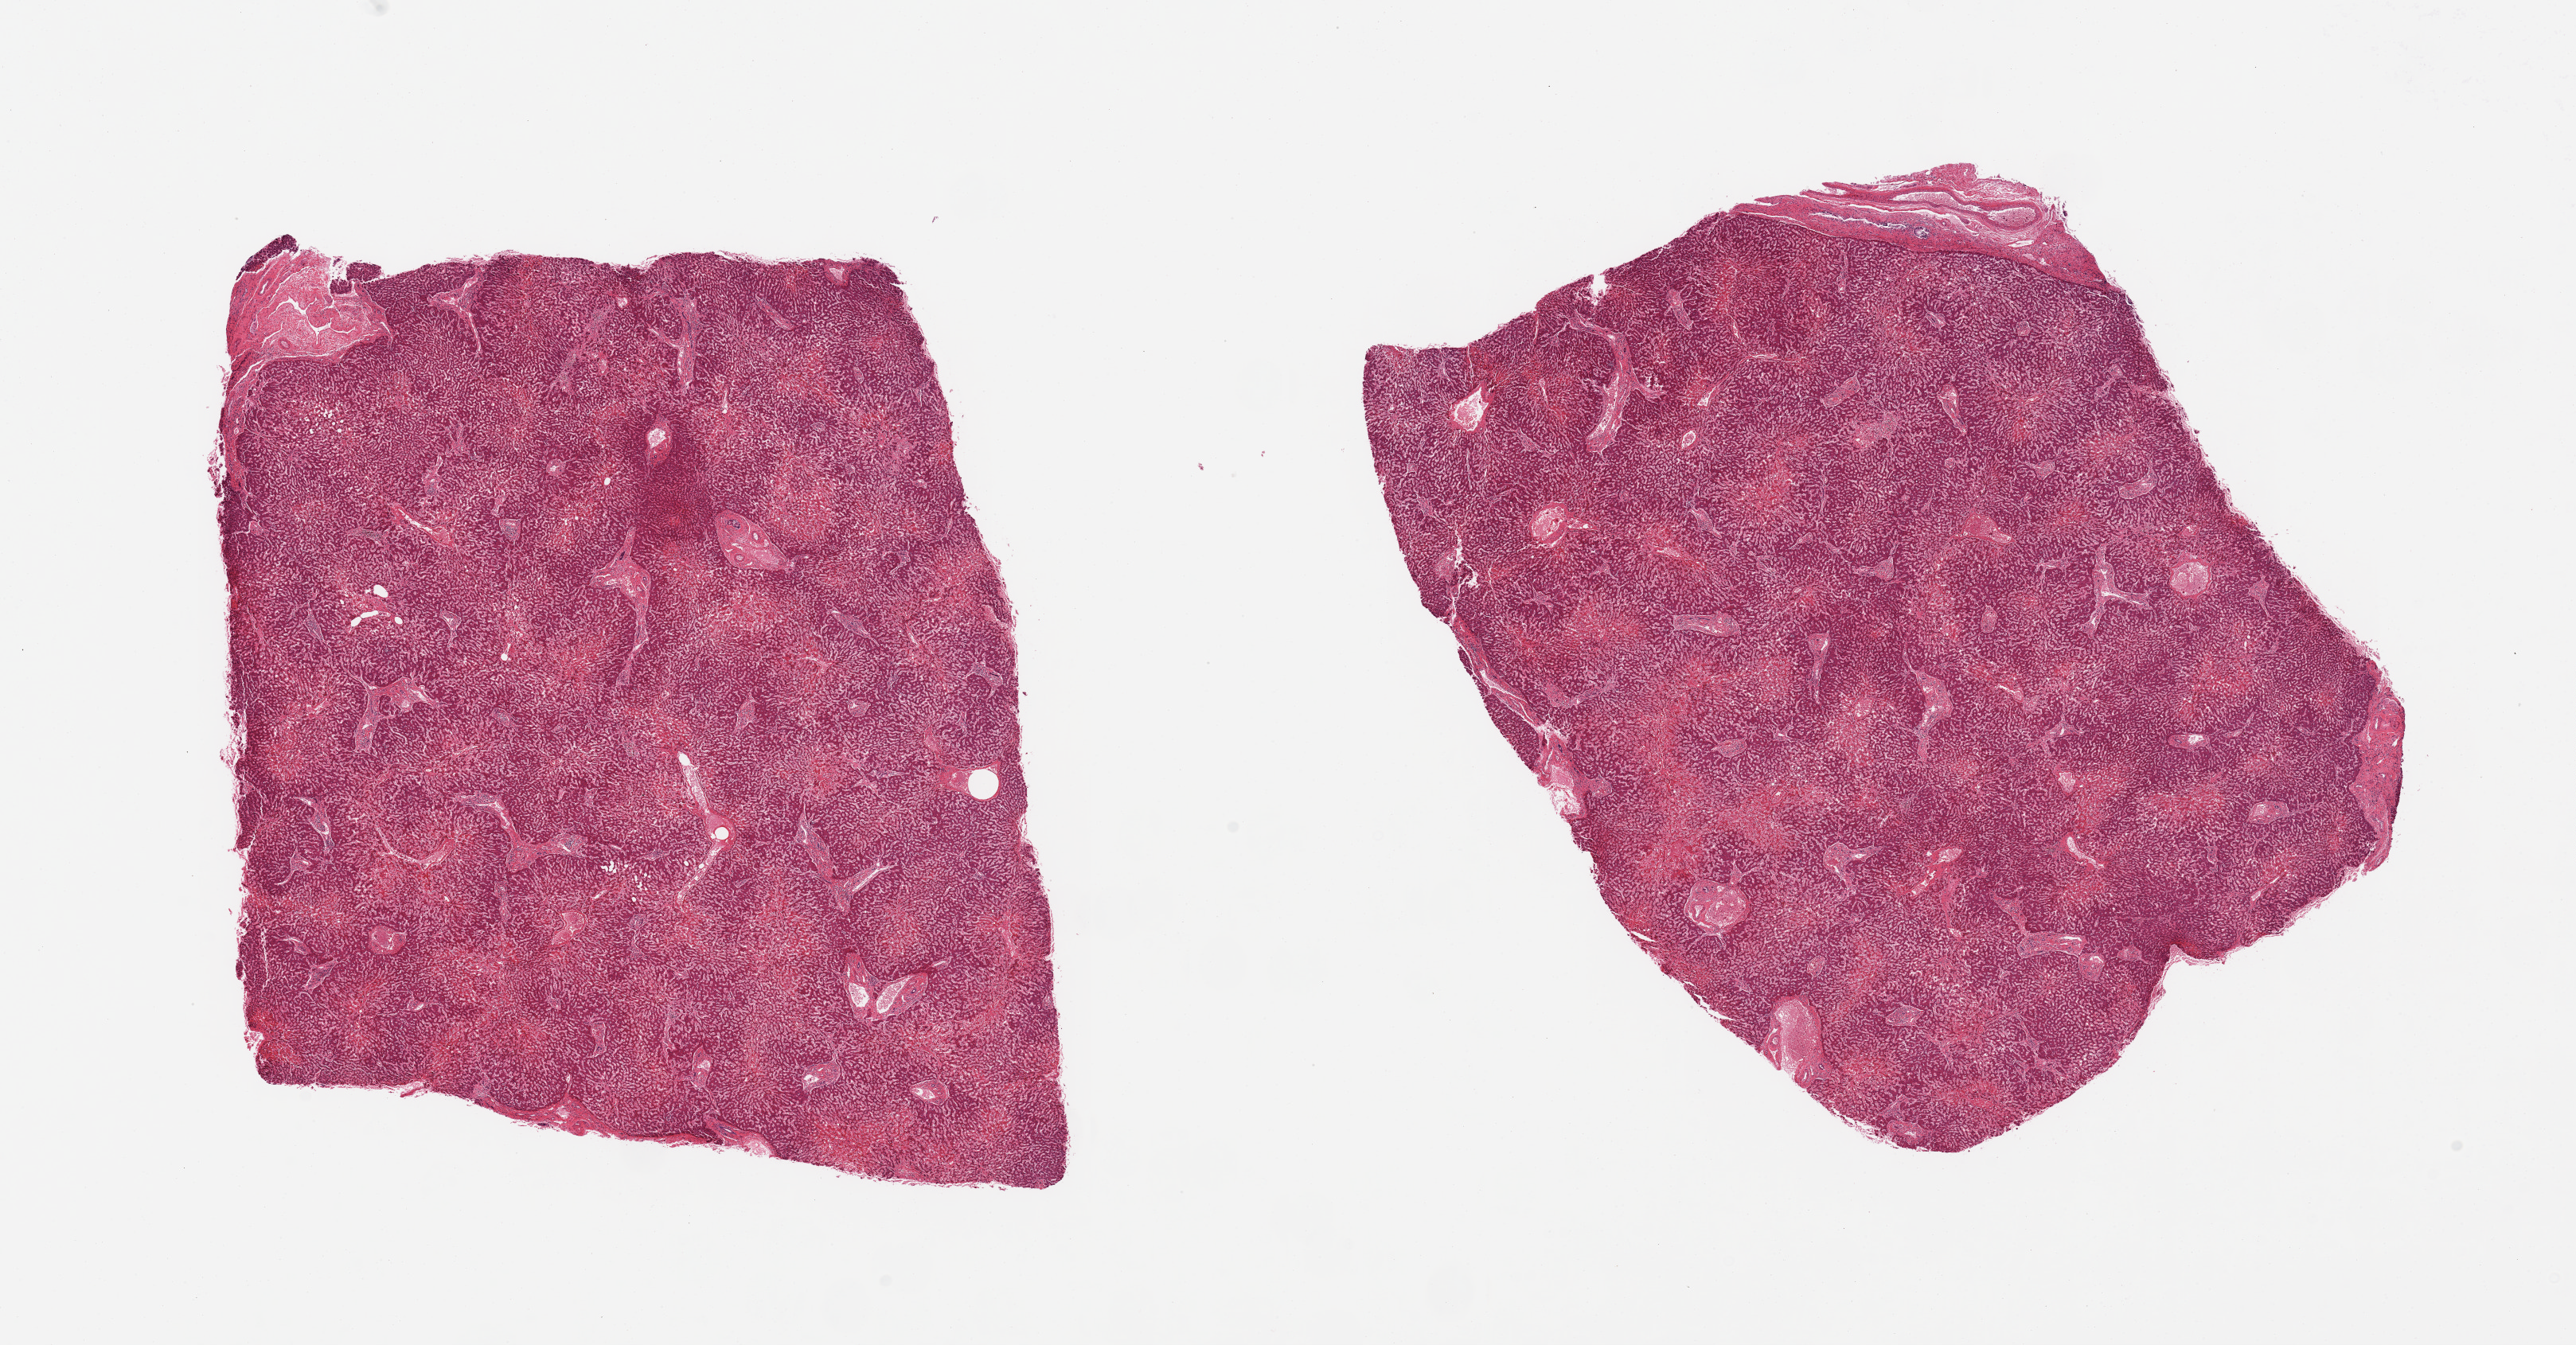
Digitized hematoxylin and eosin (H&E)-stained section — a low-resolution overview of the entire scanned area, about 25.6 x 13.4 mm (slide scanned at 20x); PAXgene-fixed paraffin-embedded (PFPE) section; target tissue: liver; donor tissue sample. Donor: male.
• pathologist's review note for this sample: 2 pieces; congestion, agonal necrosis